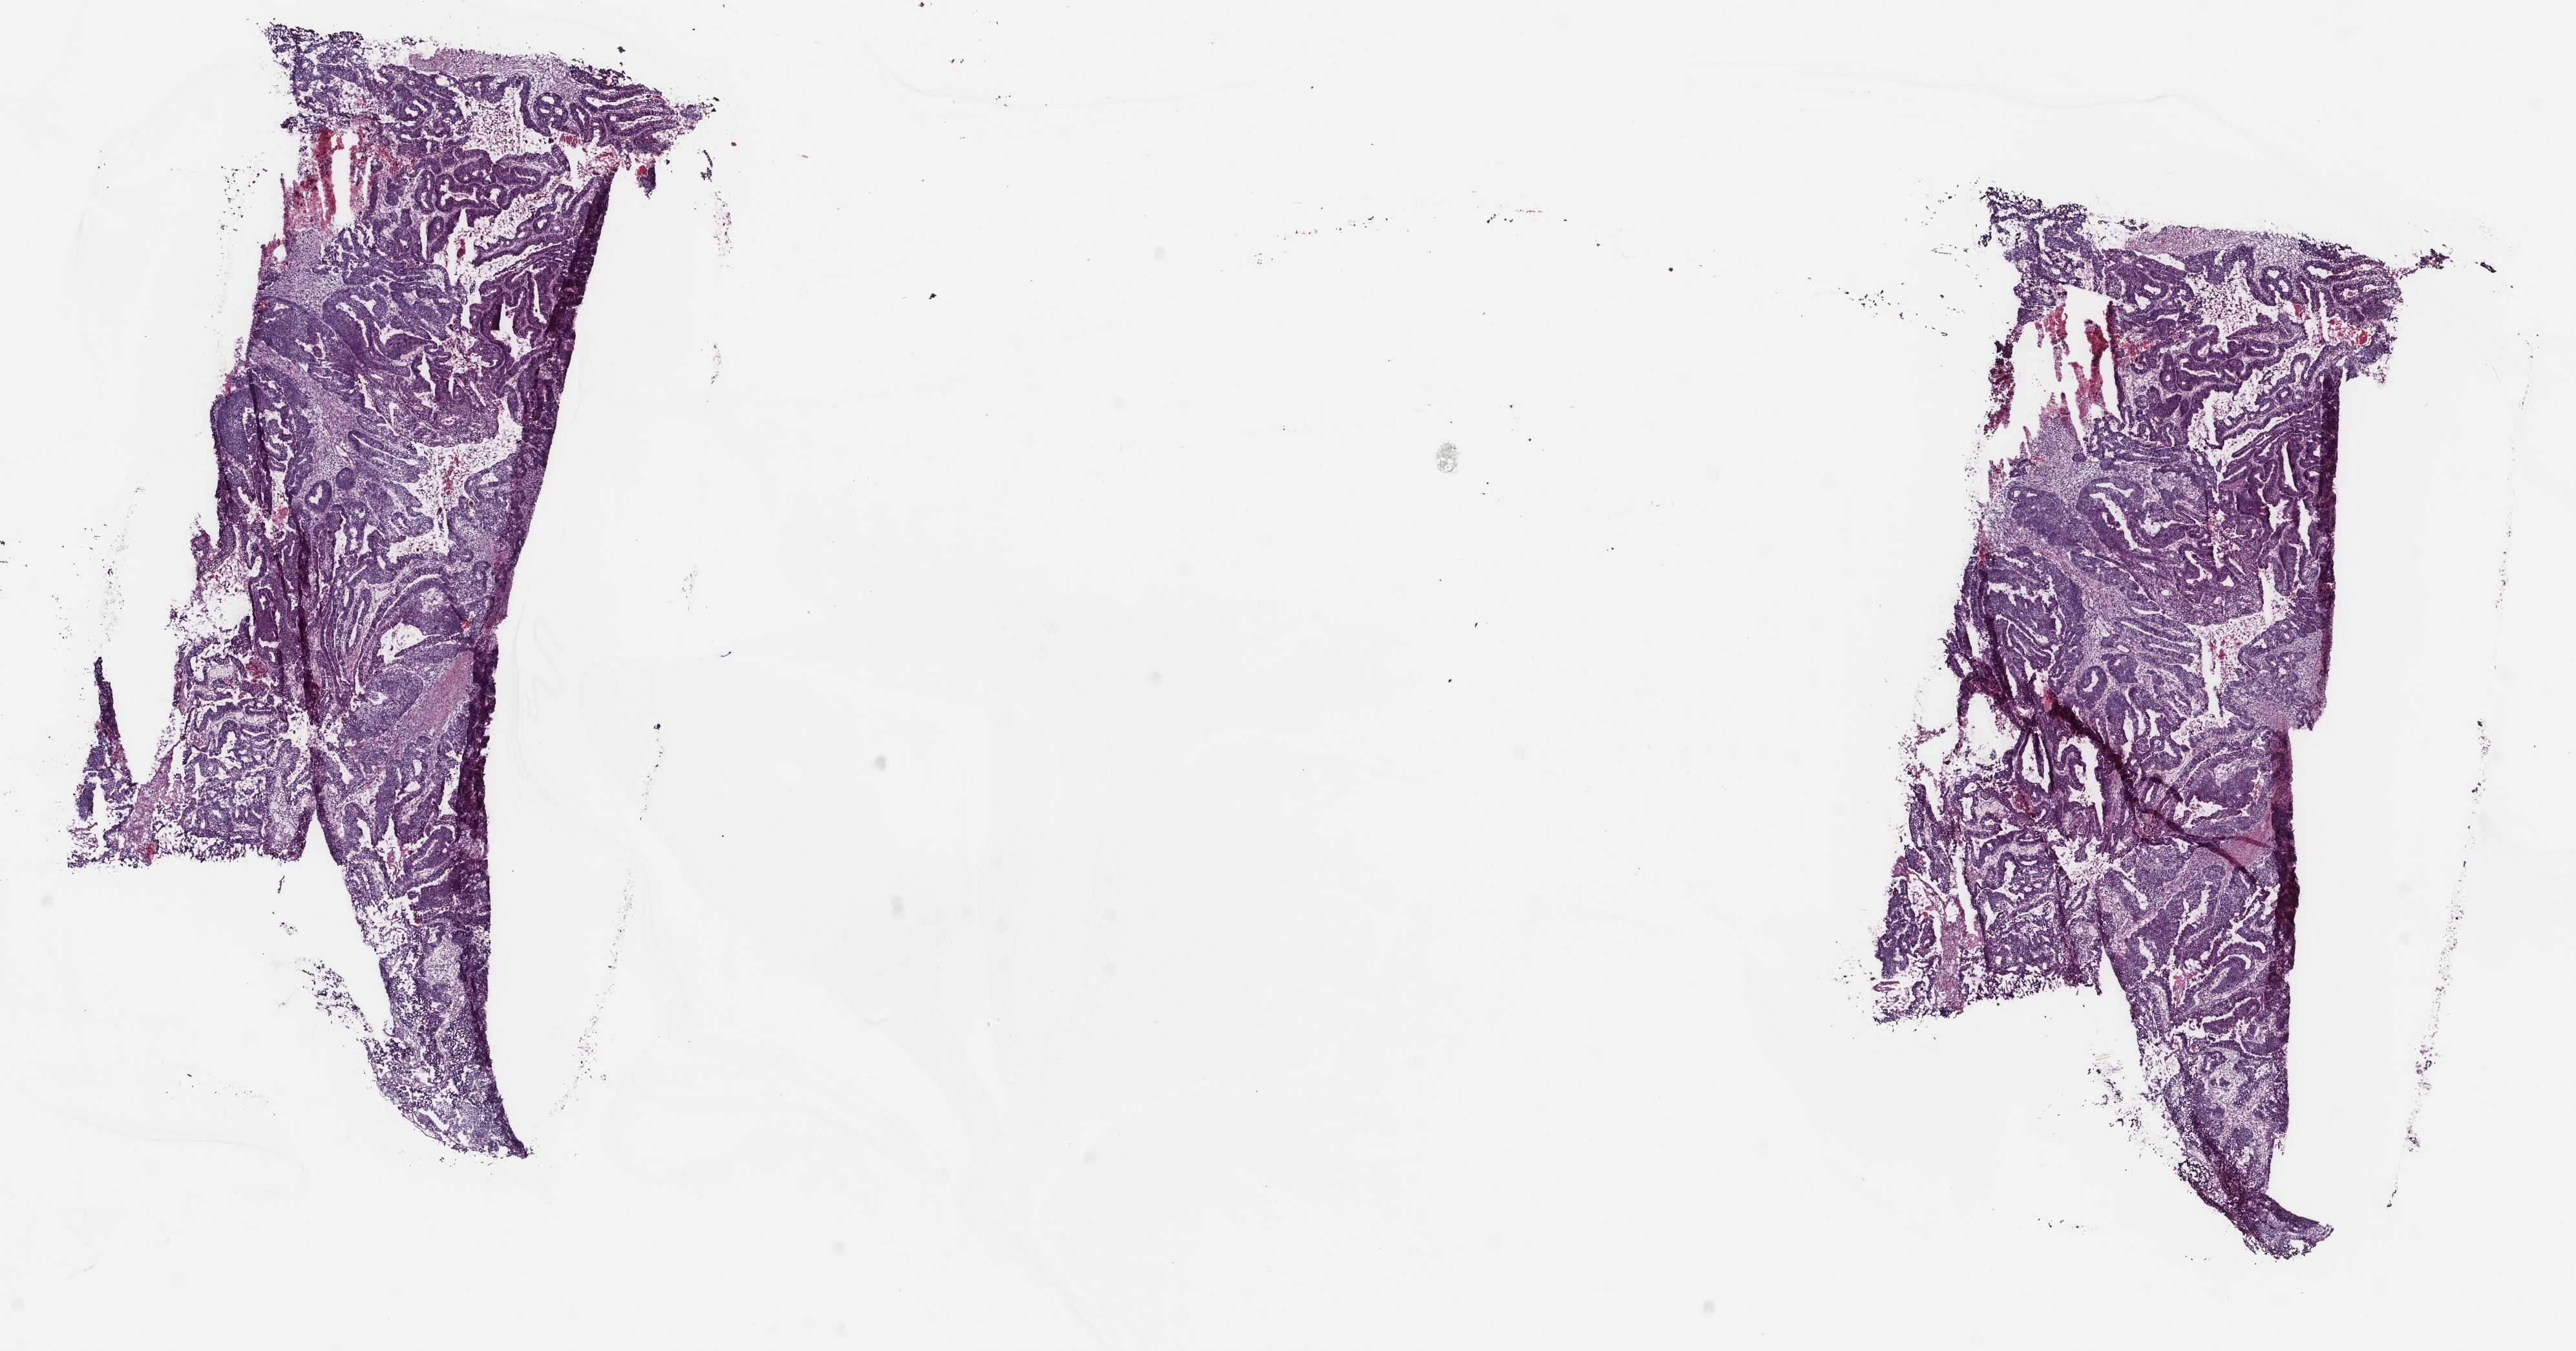
Digitized H&E-stained tissue section (whole slide), a low-resolution overview of the entire scanned area, about 15.8 x 8.3 mm, frozen section from the top of the tissue portion, primary tumour sample from the rectum. Female patient; age at initial diagnosis 47 years. Slide review estimates, as recorded: tumour cells 70%, tumour nuclei 60%, normal cells 20%, stromal cells 5%, necrosis 5%. Infiltration values recorded for this section: lymphocyte infiltration 0%, monocyte infiltration 0%, neutrophil infiltration 0%.
AJCC pathologic stage: IIA (7th edition). Histologic diagnosis: Adenocarcinoma, NOS (rectosigmoid junction). Lymph nodes positive (case pathology): 0 of 33 examined.